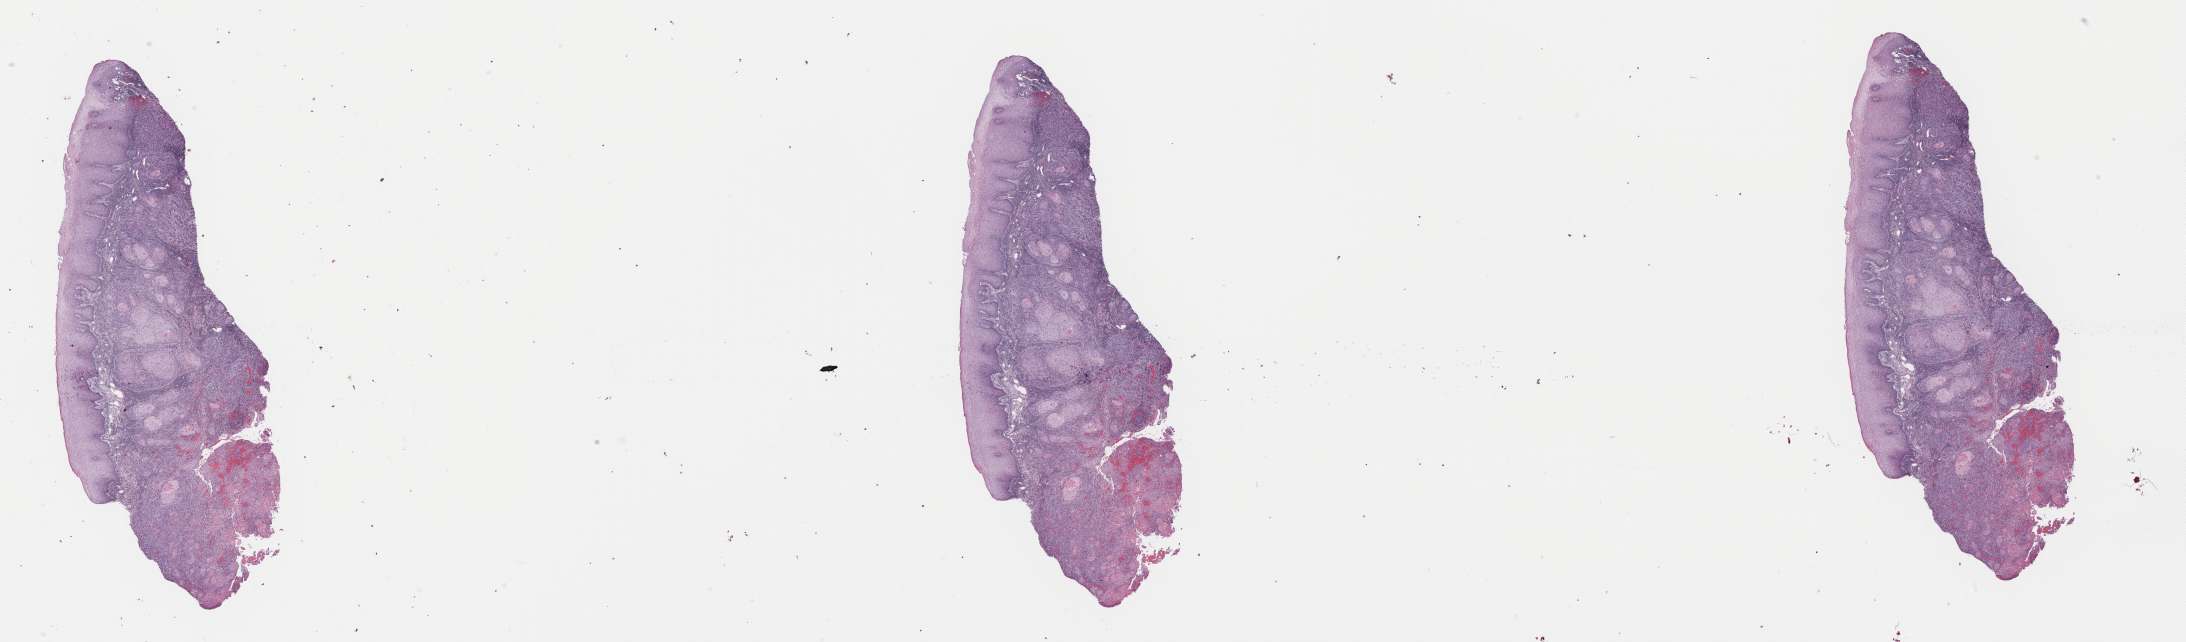
Whole-slide histology image, Hematoxylin and eosin (H&E) stained — shown as a low-resolution overview of the whole scanned area (about 34.5 x 10.1 mm, slide scanned at 40x); formalin-fixed paraffin-embedded (FFPE) diagnostic section; primary tumour sample from the head and neck. Female, age 40 years at initial diagnosis. Histologic grade: G2 (moderately differentiated).
* AJCC pathologic stage: IVA
* pathologic diagnosis: Squamous cell carcinoma, NOS (tongue, NOS)